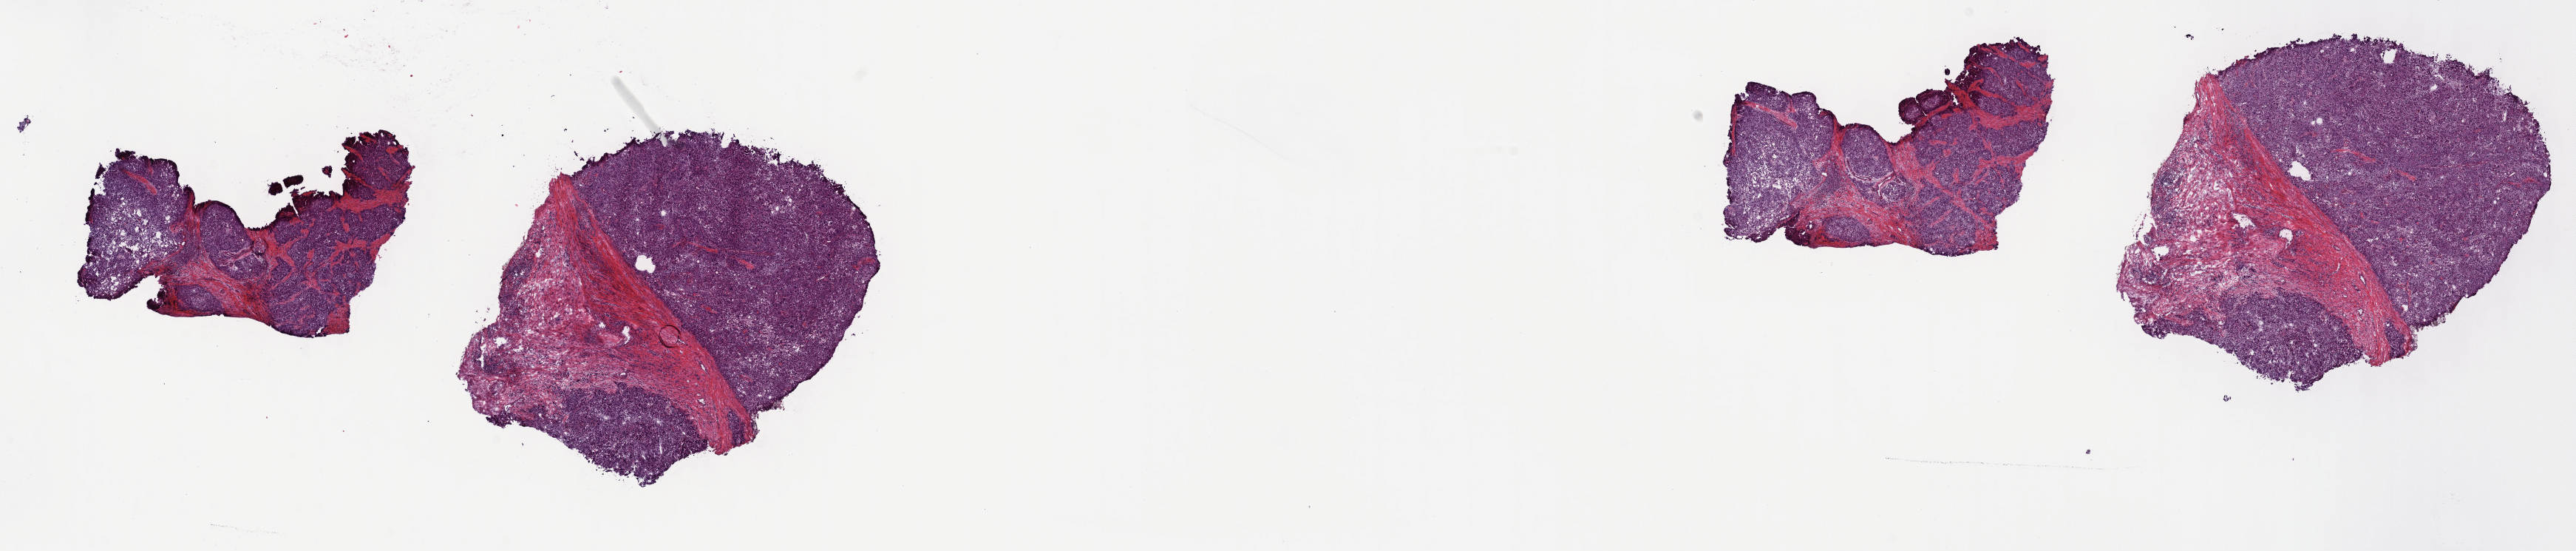
Digitized H&E tissue section (whole slide), shown as a low-resolution overview of the whole scanned area (about 28.2 x 6.0 mm, from a 40x scan), frozen section from the top of the tissue portion, sample: primary tumour, liver. Male, age 56 years at initial diagnosis. Histologic grade: G3 (poorly differentiated). Pathologist review of this section (percent, as recorded): tumour cells 75%, tumour nuclei 75%, normal cells 2%, stromal cells 22%, necrosis 1%. Inflammatory infiltration, as recorded: lymphocyte infiltration 3%, monocyte infiltration 1%, neutrophil infiltration 4%.
* AJCC pathologic stage: II (6th edition)
* pathologic diagnosis: Hepatocellular carcinoma, NOS
* TNM: T2 N0 M0